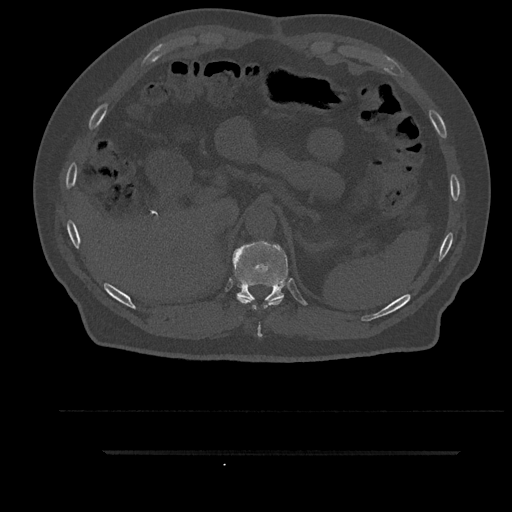
CT including the spine, one axial slice. Position 331 of 797 along the scan axis. Reconstruction kernel Br40s/3. Bone window (W 1800 / L 400 HU). 512 × 512 image matrix, field of view 432 × 432 mm. Male patient, age 63 years. From the clinical record (not read from this slice): primary cancer: renal; vertebrae with lytic lesions (as recorded): T8.
Annotated regions visible in this slice (semi-automatic segmentation, software-assisted and operator-edited):
- T10 vertebra: box from (x=237, y=297) to (x=284, y=337) px
- T11 vertebra: (x=232, y=241)–(x=288, y=302)